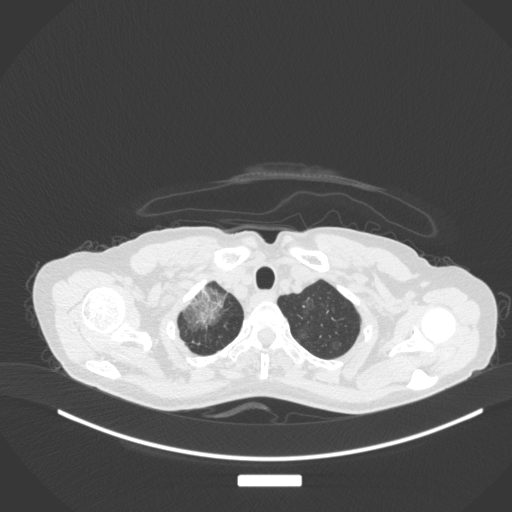
Chest CT, one axial slice. 120 kVp. Lung window (W 1500 / L -600 HU). 512 × 512 image matrix, field of view 400 × 400 mm. Female patient, age 59 years. From the clinical record (not read from this slice): clinical TNM (as recorded): T3 N0 M0; histopathological grade: G1.
Outlined on this slice (bounding box drawn by a radiologist):
- lung tumour (recorded histology: adenocarcinoma): bounding box <176,283,223,328> (left, top, right, bottom; pixels)